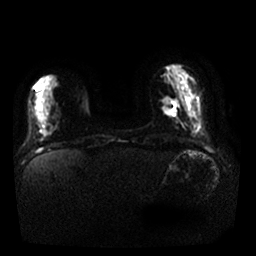
Breast MRI, one axial slice. Slice 6 of 25 in the series (ordered by position). Diffusion-weighted series; image 2 of 4 stored at this slice position (different b-values; order by instance number). 1.5 T. 4 mm slice thickness. 256 × 256 image matrix. Female patient.
Annotated regions visible in this slice (expert manual segmentation):
- tumour on diffusion-weighted imaging: bounding box [x1, y1, x2, y2] px = [162, 98, 178, 115]